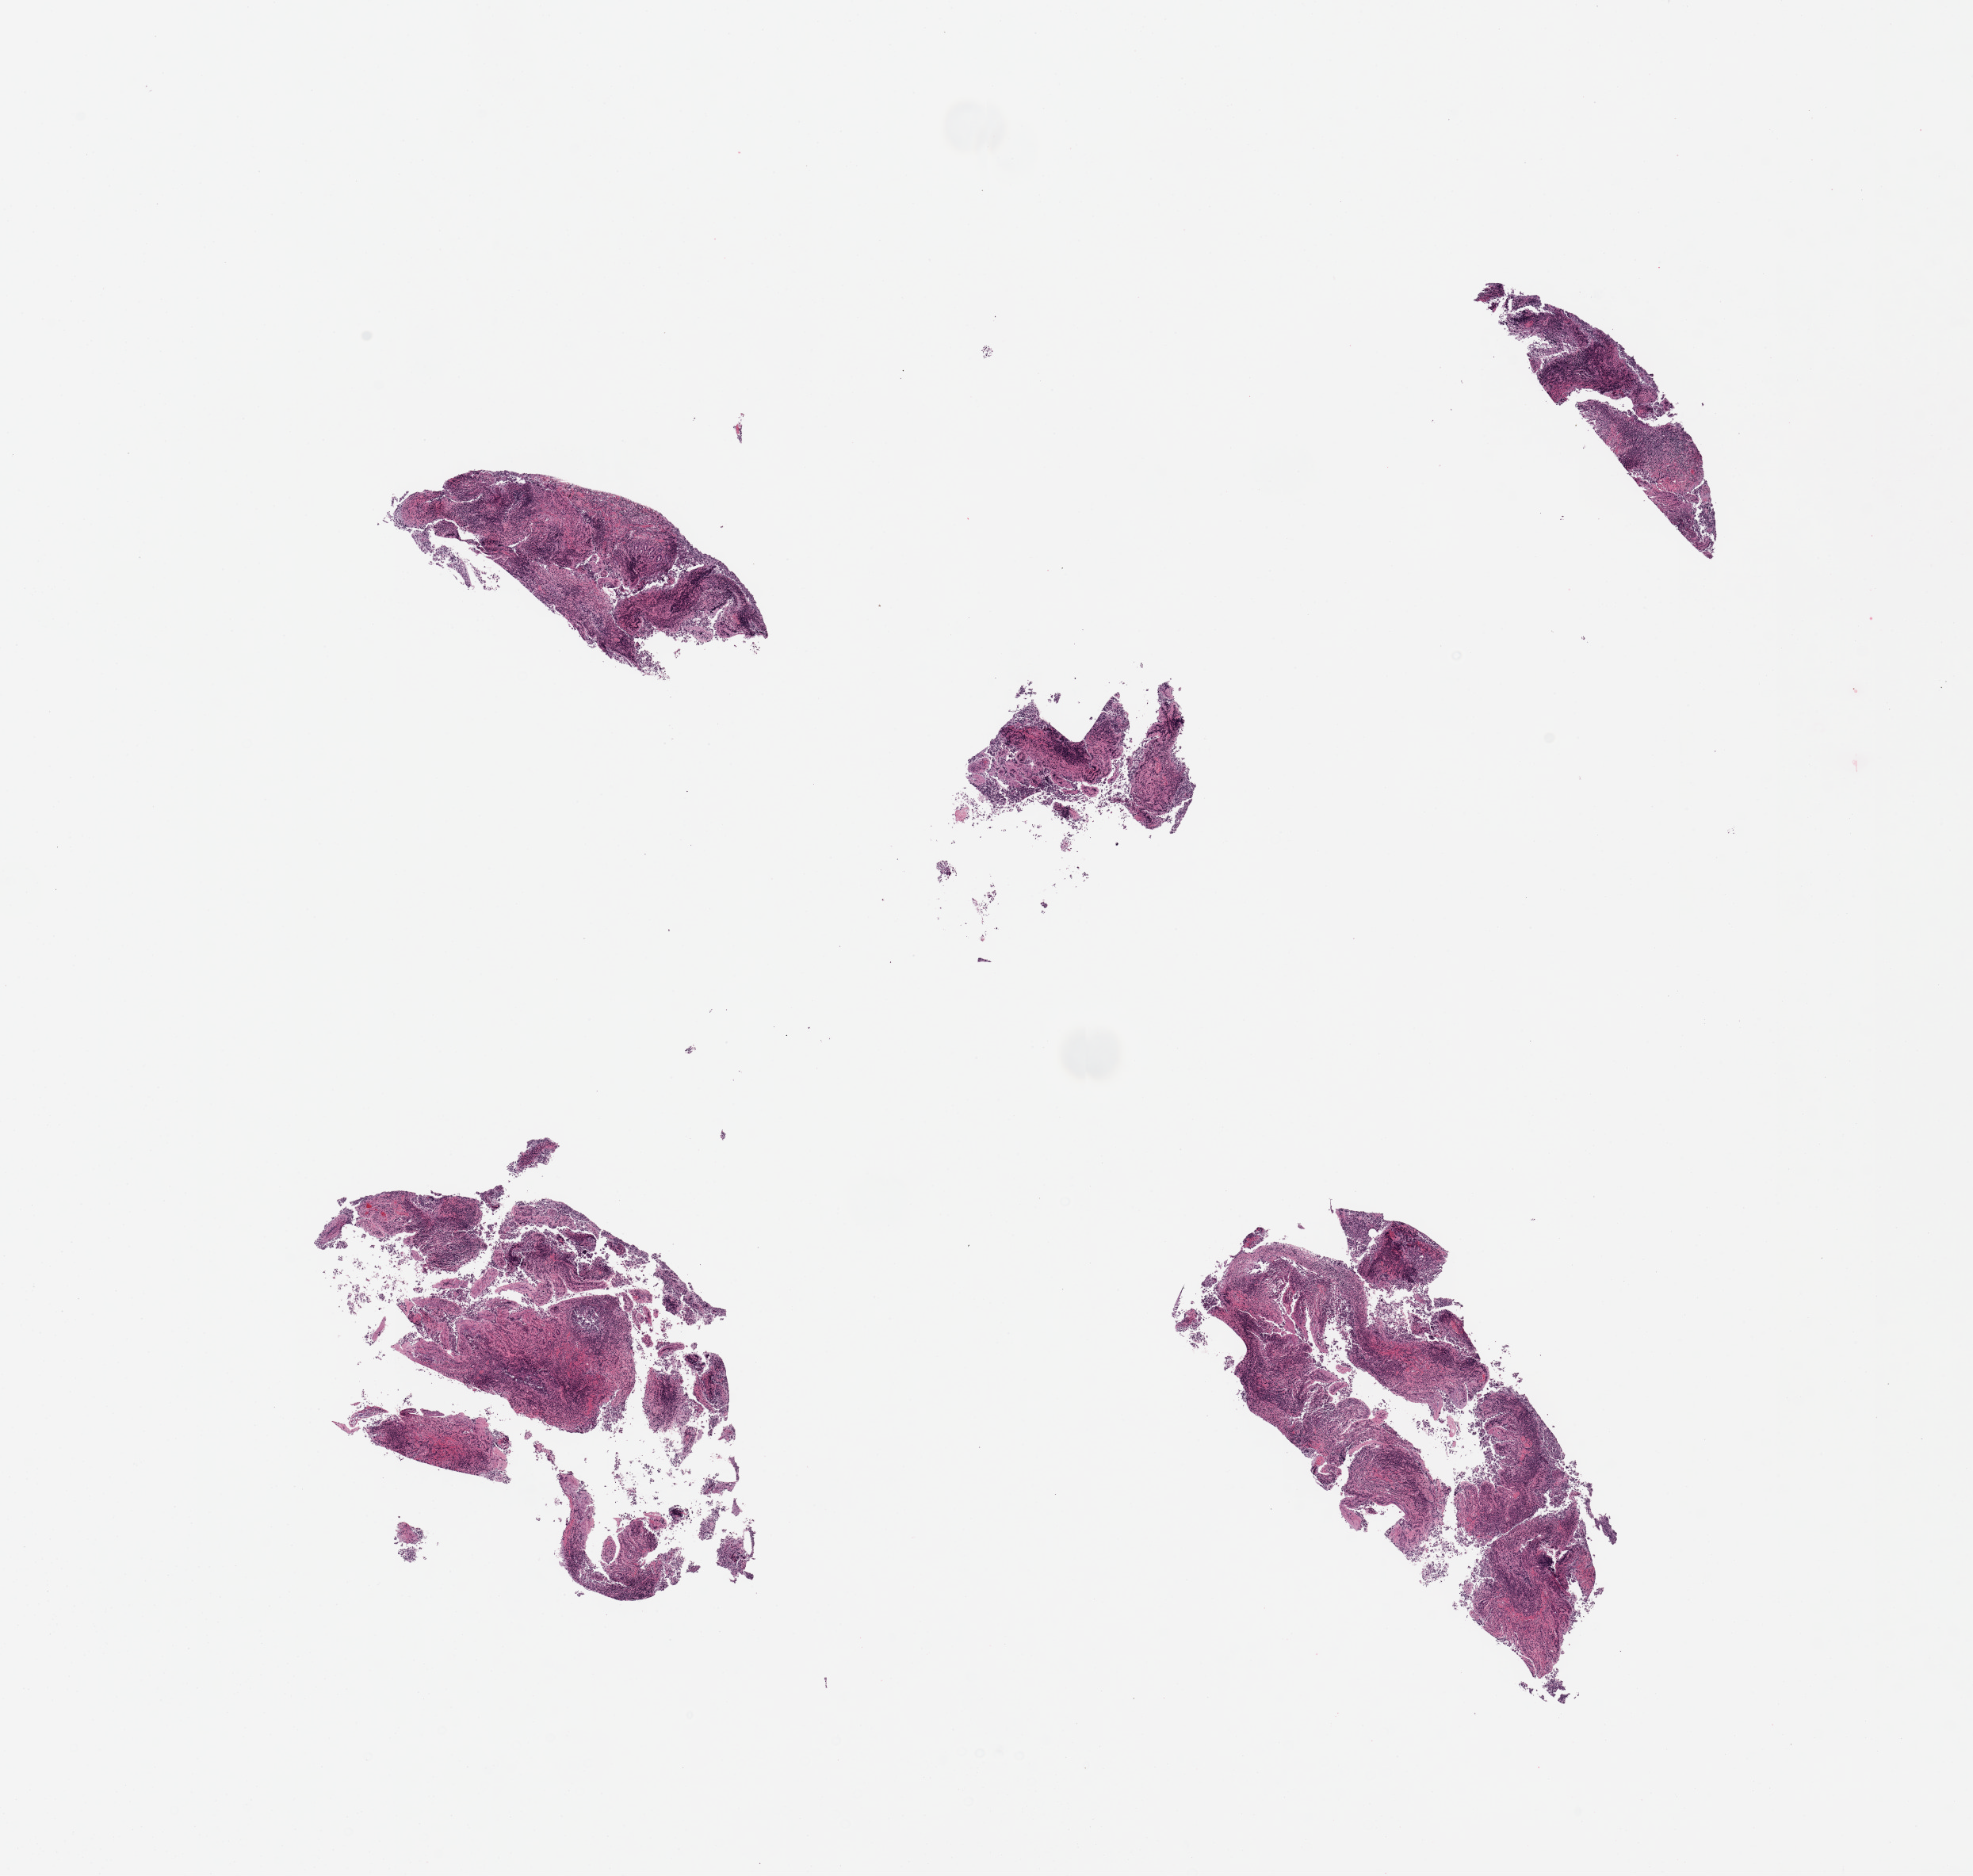
Haematoxylin and eosin whole-slide image — whole scanned area (about 19.7 x 18.7 mm, acquisition: 20x scan) shown as a low-resolution overview, PAXgene-fixed paraffin-embedded (PFPE) section, section of ileum (target tissue), tissue donor sample. Male donor.
Review note (as recorded): 5 pieces; lymphoid tissue is generally diffusely distributed in mucosa.